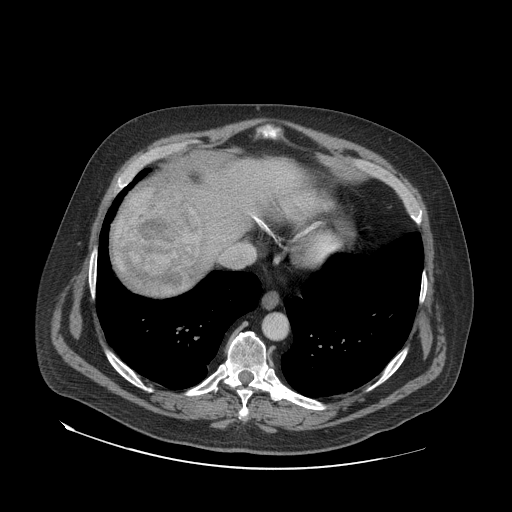
Contrast-enhanced abdominal CT (liver protocol), one axial slice; slice 67 of 79 in the series (ordered by position); reconstruction kernel STANDARD; 140 kVp; soft-tissue window (W 400 / L 40 HU); 512 × 512 image matrix, field of view 480 × 480 mm. From the clinical record (not read from this slice): diagnosis: hepatocellular carcinoma (patient treated with transarterial chemoembolisation; whether this scan precedes or follows treatment is not stated here); TNM stage (as recorded): Stage-IVA; Child-Pugh class: A; tumour differentiation: well differentiated.
Structures marked on this image (semi-automatically segmented with operator editing):
- abdominal aorta: bounding box (x1, y1, x2, y2) in pixels: (264, 314, 286, 338)
- liver parenchyma outside the tumour (the mass and vessels are separate outlines, so this box may not span the whole liver): (112, 152, 320, 296)
- mass: (116, 185, 203, 289)
- liver vessels: (252, 215, 261, 223)